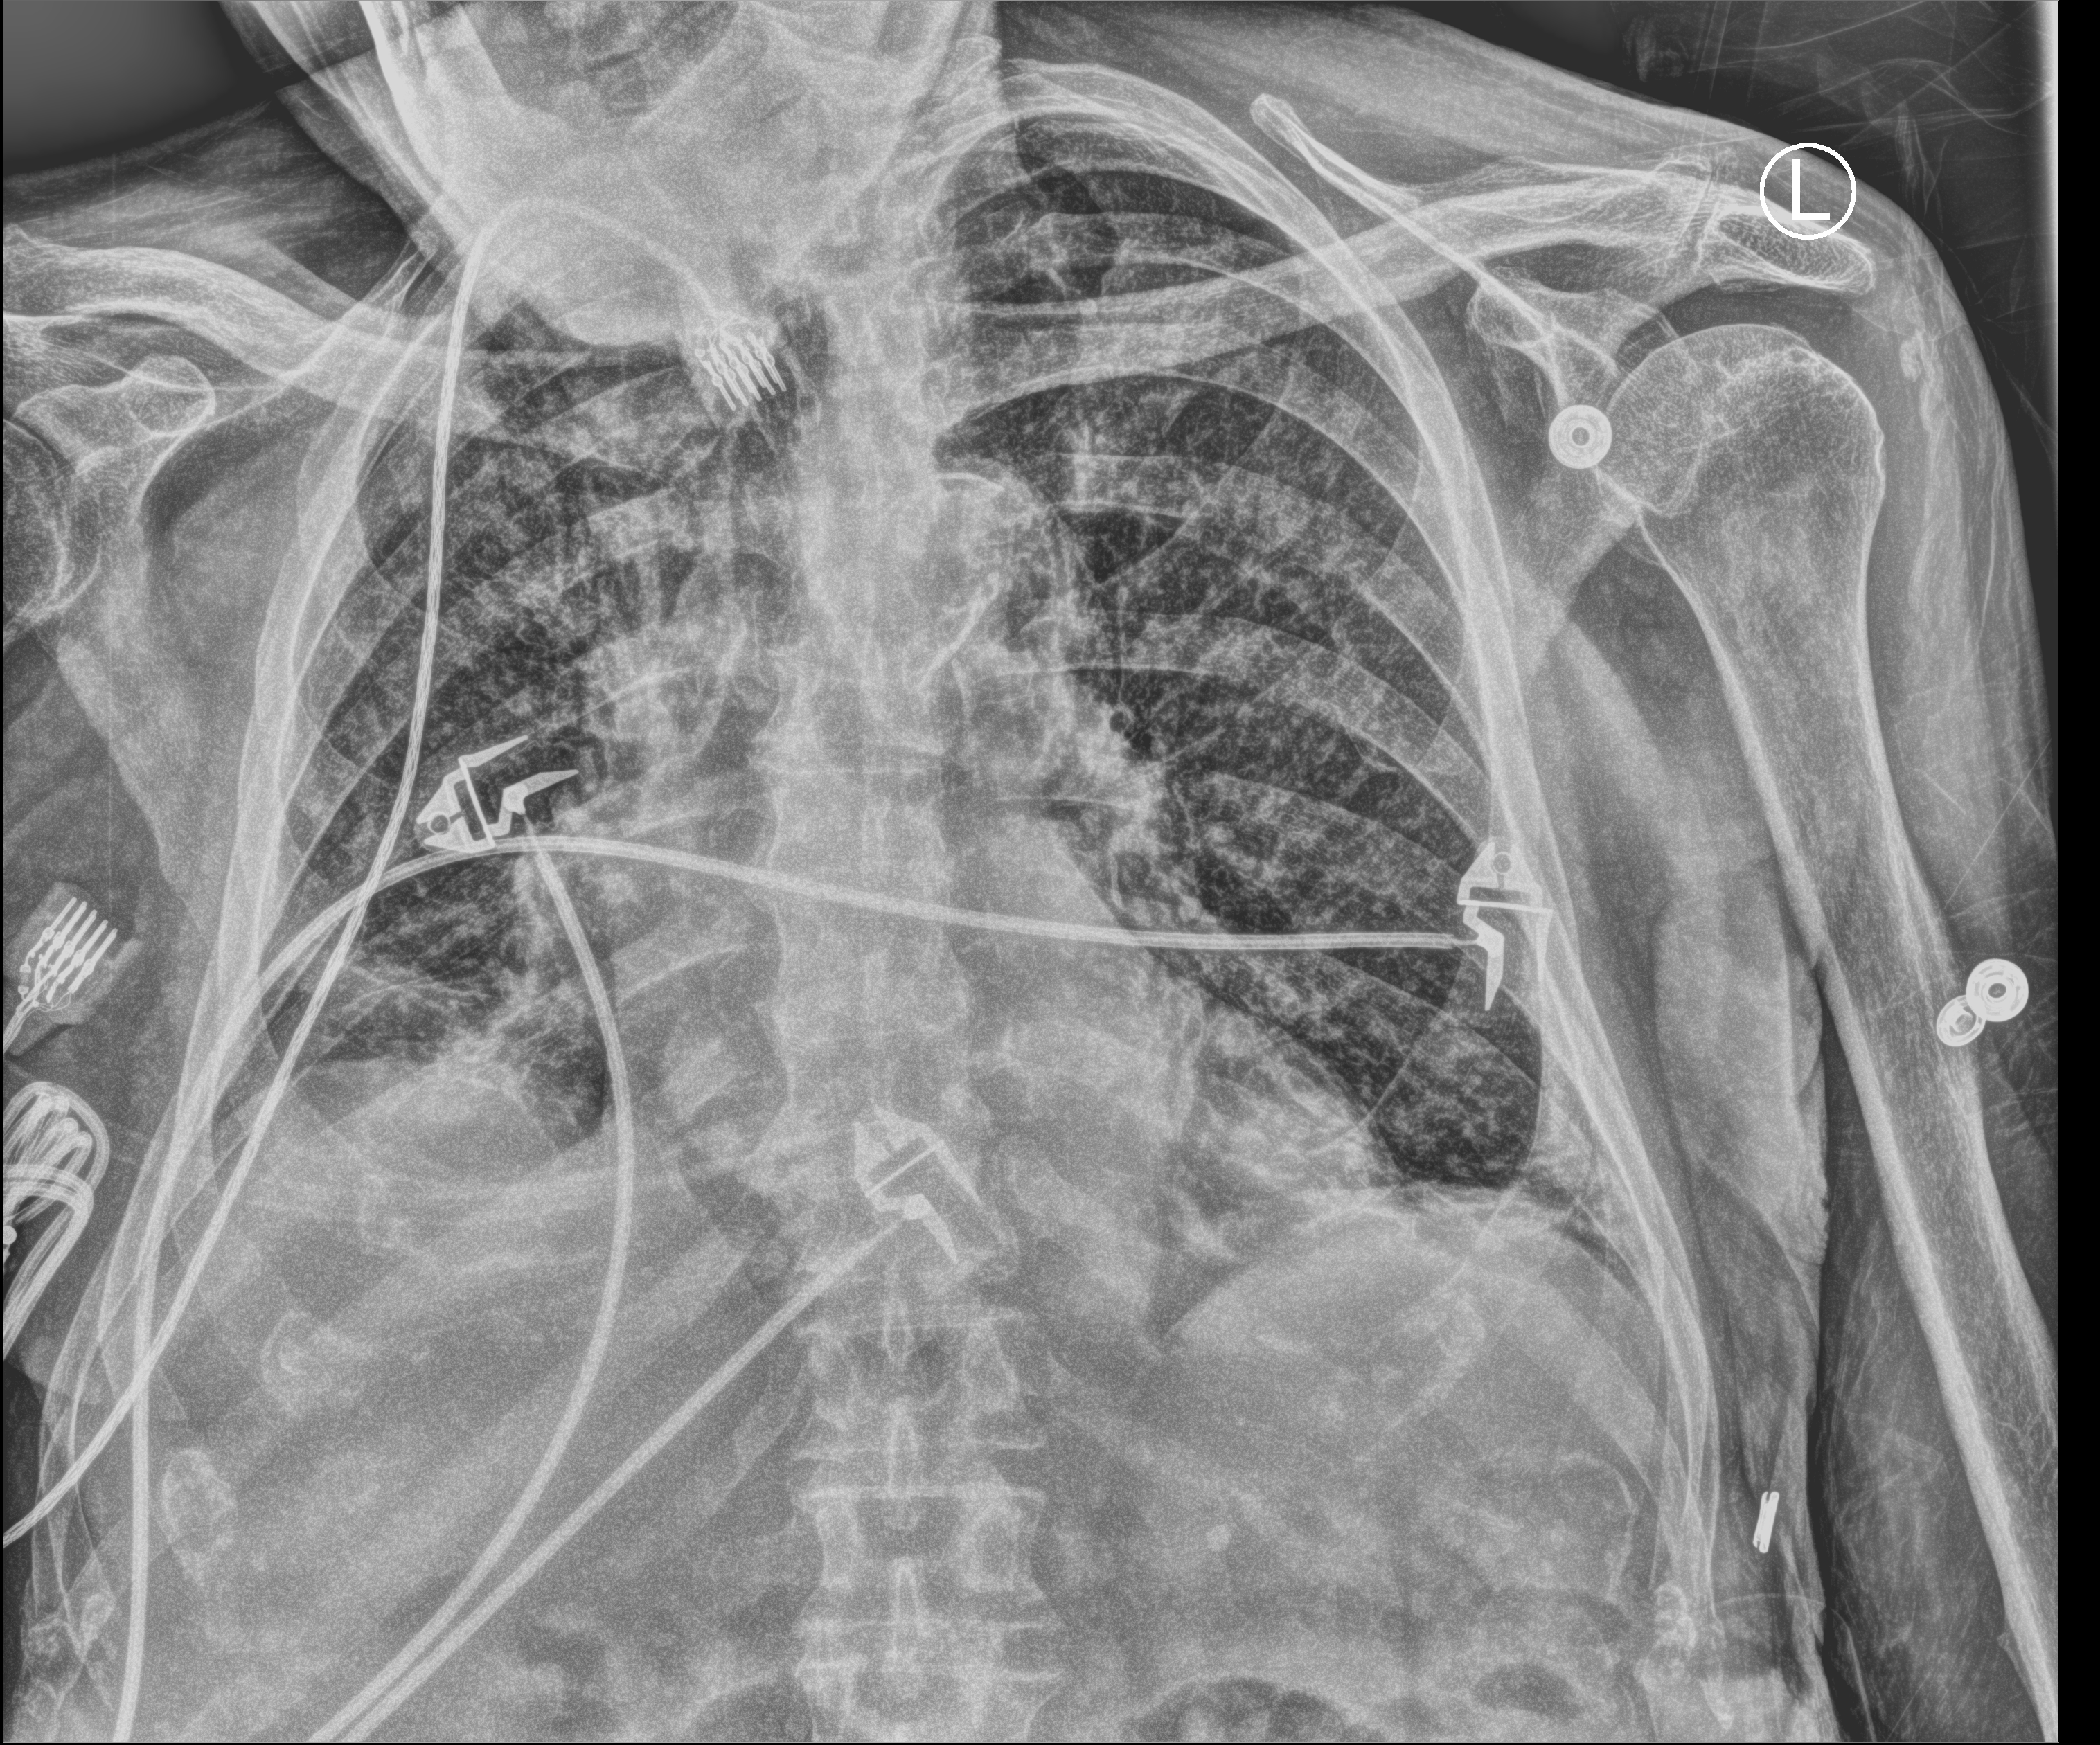
Portable chest radiograph, anteroposterior (AP) projection. Male patient hospitalised with COVID-19, age 75–90 years.
Hospital-stay facts (about this admission, not read from this image; timing relative to this image not recorded): smoking status (admission record): never; mechanically ventilated during this hospital stay: yes; length of hospital stay: 28 days.